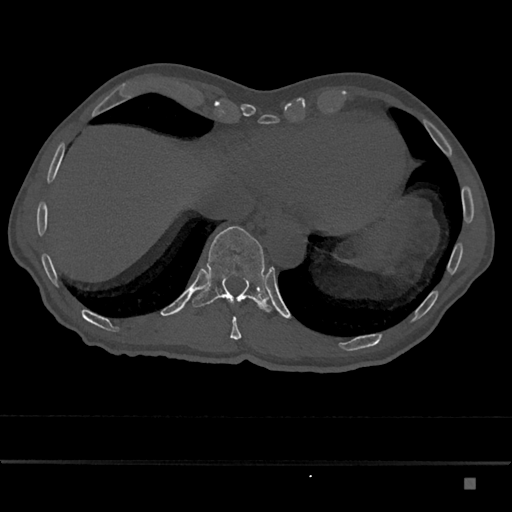
CT including the spine, one axial slice; slice 697 of 797 in the series (ordered by position); reconstruction kernel Br40s/3; bone window (W 1800 / L 400 HU); 512 × 512 image matrix, field of view 390 × 390 mm. Patient: male, 72 years. Case-level facts recorded for this patient, not image findings: primary cancer: prostate.
Annotated regions visible in this slice (semi-automatic segmentation, software-assisted and operator-edited):
- T10 vertebra: box from (x=229, y=300) to (x=242, y=340) px
- T11 vertebra: (x=192, y=226)–(x=272, y=312)